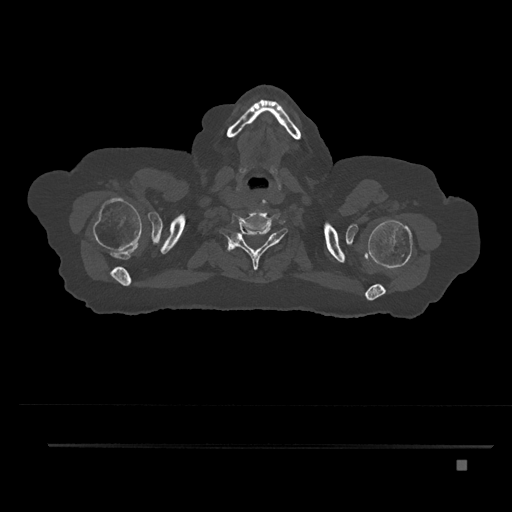
CT including the spine, one axial slice; slice 727 of 797 in the series (ordered by position); reconstruction kernel Br40s/3; bone window (W 1800 / L 400 HU); 512 × 512 image matrix, field of view 437 × 437 mm. Patient: female, 76 years. Case-level facts recorded for this patient, not image findings: primary cancer: lung.
Structures marked on this image (semi-automatic segmentation, software-assisted and operator-edited):
- T1 vertebra: bounding box (x1, y1, x2, y2) in pixels: (228, 240, 250, 255)